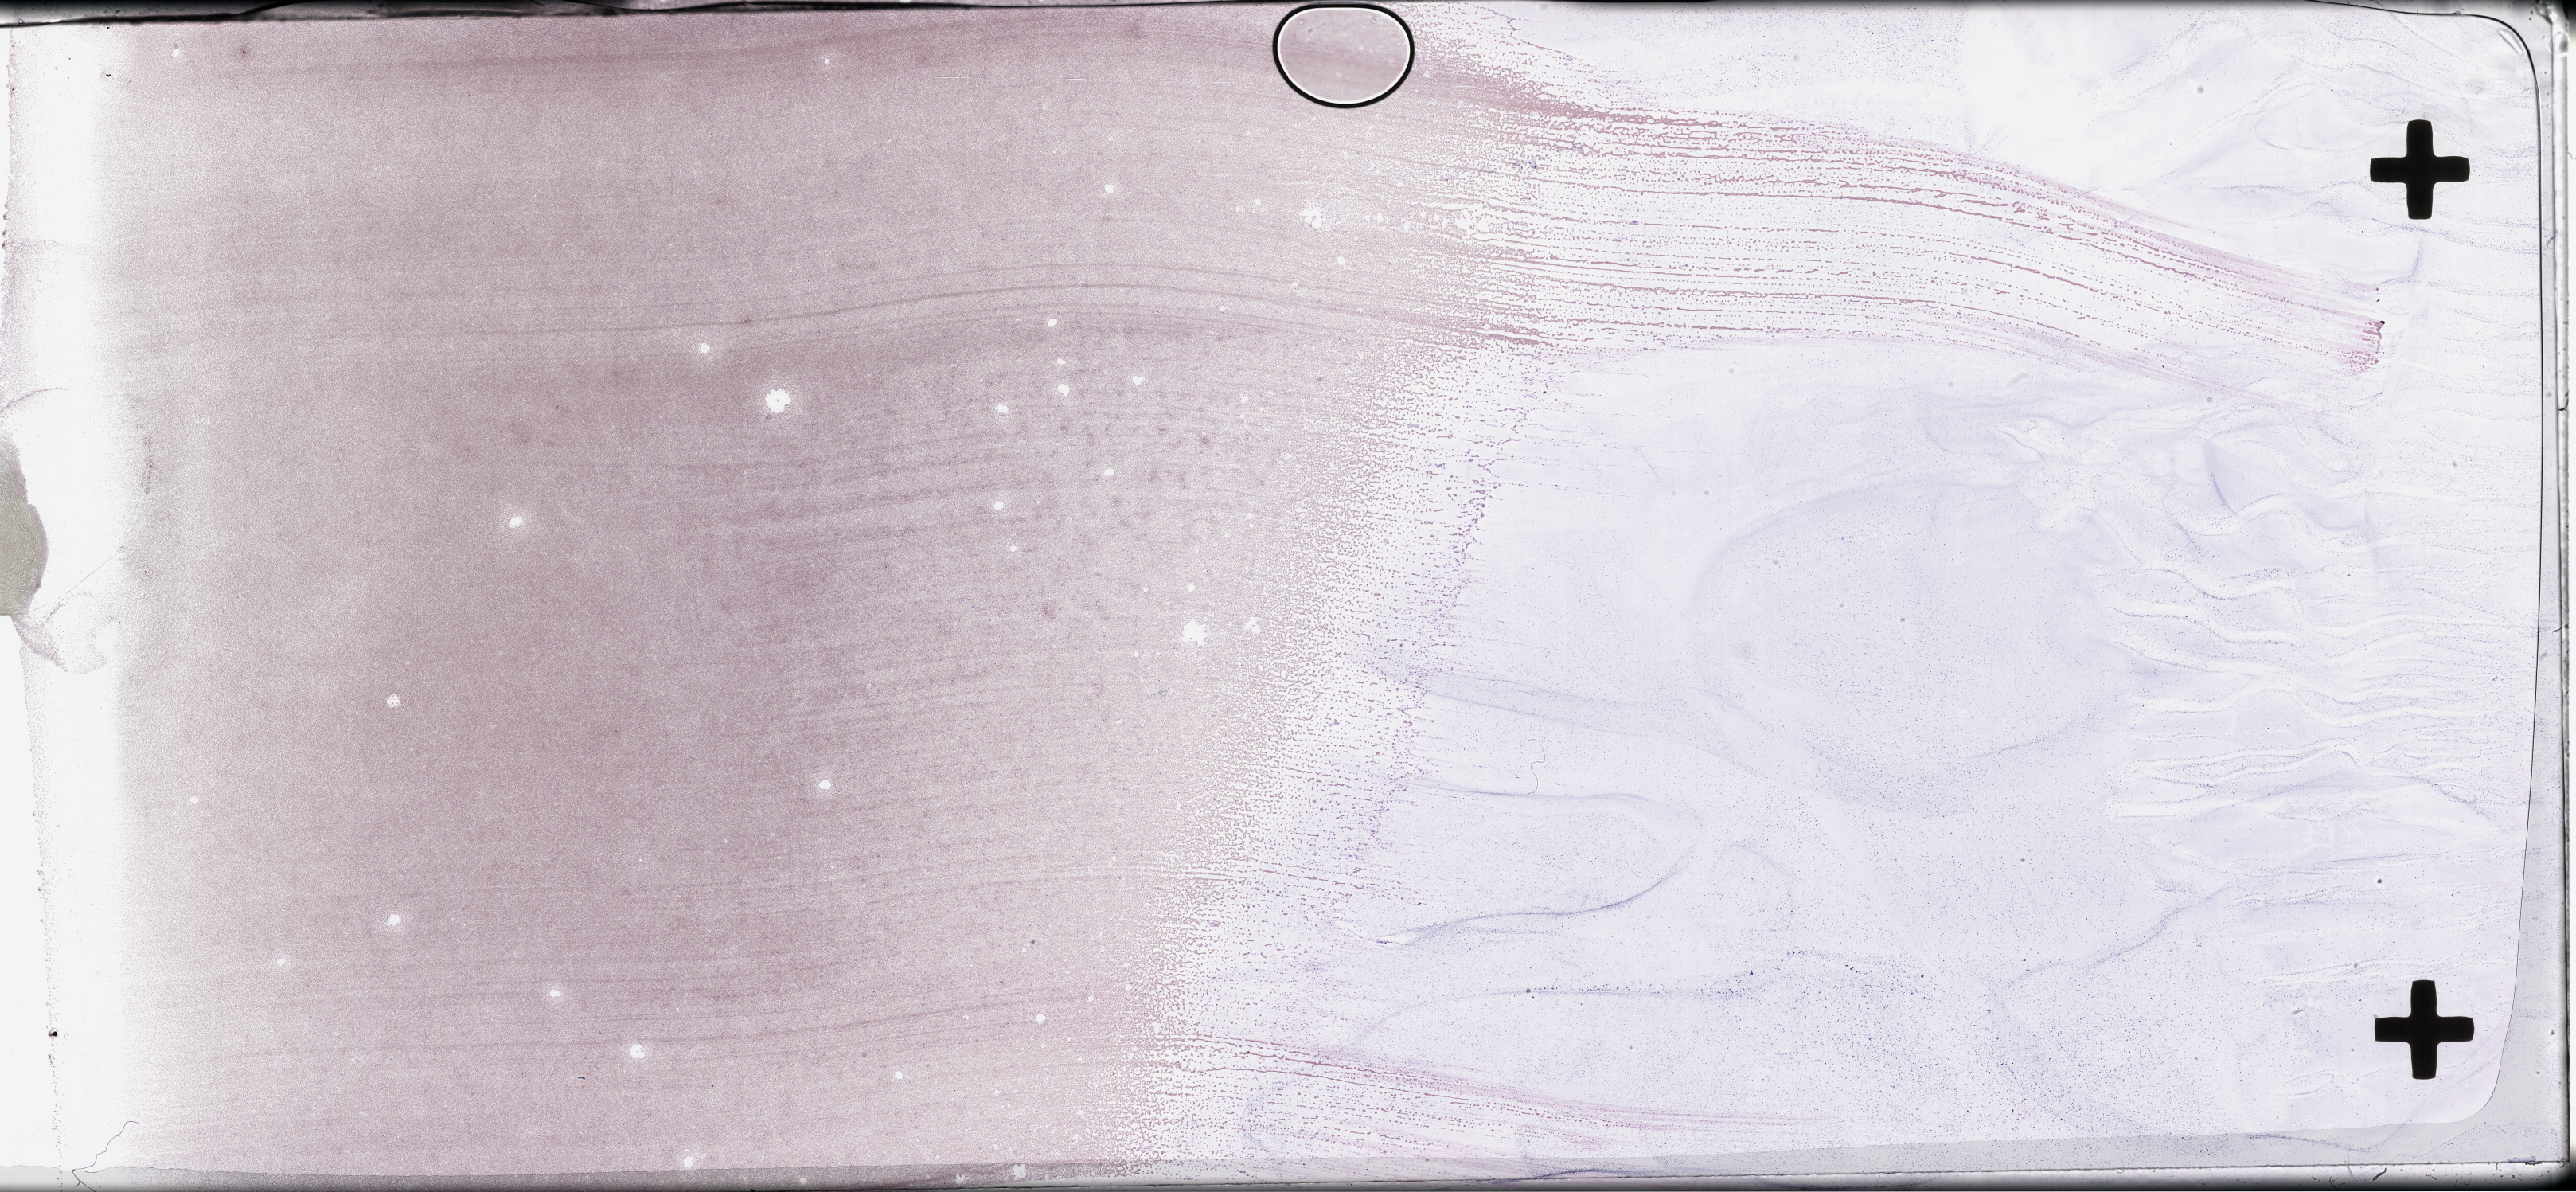
Whole-slide image of a bone marrow smear, Wright-Giemsa stain — whole scanned area (about 52.3 x 24.2 mm) shown as a low-resolution overview, smear from an EDTA sample, collected on treatment. Female patient.
Patient diagnosis: Plasma Cell Myeloma.